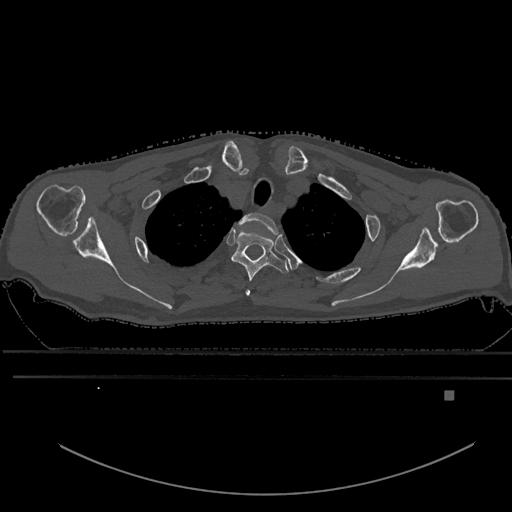
CT including the spine, one axial slice; slice 499 of 969 in the series (ordered by position); bone window (W 1800 / L 400 HU); 0.5 mm slice thickness; 512 × 512 image matrix, field of view 456 × 456 mm. Patient: male, 82 years. Case-level facts recorded for this patient, not image findings: primary cancer: prostate; vertebrae with lytic lesions (as recorded): T11, T9, T8, T2.
Outlined on this slice (semi-automatically segmented with operator editing):
- T1 vertebra: bounding box [x1, y1, x2, y2] px = [238, 212, 278, 234]
- T2 vertebra: [231, 229, 289, 295]